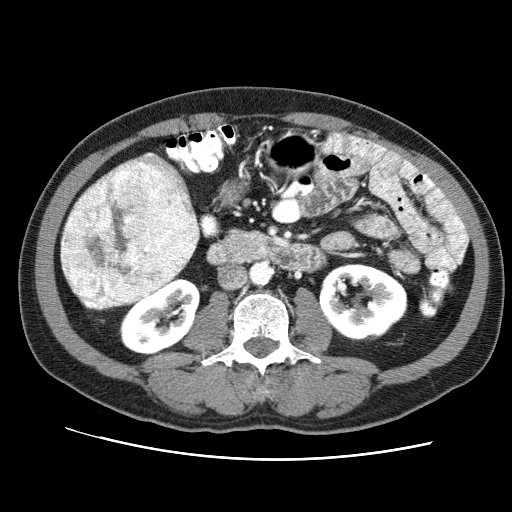
Contrast-enhanced abdominal CT (liver protocol), one axial slice; slice 20 of 71 in the series (ordered by position); reconstruction kernel STANDARD; 120 kVp; soft-tissue window (W 400 / L 40 HU); 512 × 512 image matrix, field of view 360 × 360 mm. Case-level facts recorded for this patient, not image findings: diagnosis: hepatocellular carcinoma (patient treated with transarterial chemoembolisation; whether this scan precedes or follows treatment is not stated here); TNM stage (as recorded): Stage-II; Child-Pugh class: A; tumour nodularity: multinodular.
Annotated regions visible in this slice (semi-automatic segmentation, software-assisted and operator-edited):
- liver parenchyma outside the tumour (the mass and vessels are separate outlines, so this box may not span the whole liver): box from (x=60, y=152) to (x=199, y=310) px
- mass: (x=60, y=160)–(x=199, y=309)
- liver vessels: (x=147, y=153)–(x=163, y=170)